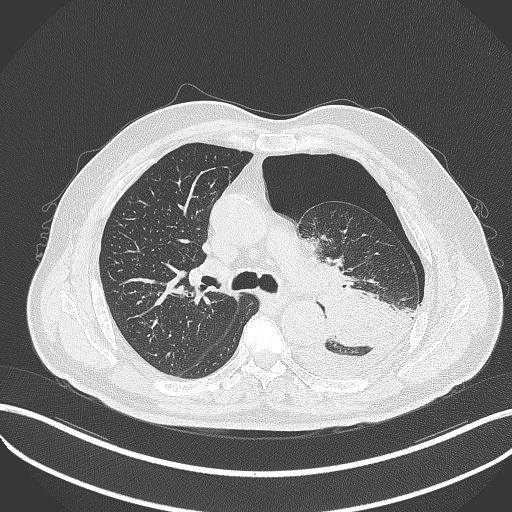
Chest CT, one axial slice. Position 333 of 464 along the scan axis. Reconstruction kernel B70f. 120 kVp. Lung window (W 1500 / L -600 HU). 1 mm slice thickness. 512 × 512 image matrix, field of view 400 × 400 mm. Male patient, age 76 years. From the clinical record (not read from this slice): clinical TNM (as recorded): T3 N0 M1b.
Outlined on this slice (rectangle marked by the reading radiologist):
- lung tumour (recorded histology: adenocarcinoma): bounding box <319,285,398,345> (left, top, right, bottom; pixels)